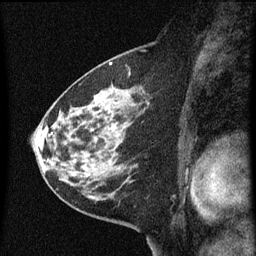
Breast MRI (dynamic contrast-enhanced), one sagittal slice. Position 32 of 60 along the scan axis. Dynamic contrast-enhanced series, image 2 of 3 at this slice position (ordered by acquisition). 1.5 T. TE 4.2 ms, TR 8 ms. 2 mm slice thickness. 256 × 256 image matrix, field of view 180 × 180 mm. Patient: female, 60 years.
Outlined on this slice (semi-automatically segmented with operator editing):
- analysis volume of interest (the breast-tissue region the enhancement analysis was run in; not a lesion): bounding box (x1, y1, x2, y2) in pixels: (48, 82, 151, 183)
- tumour enhancement mask (voxels above the 70 % enhancement threshold inside the analysis volume of interest): (50, 104, 115, 177)